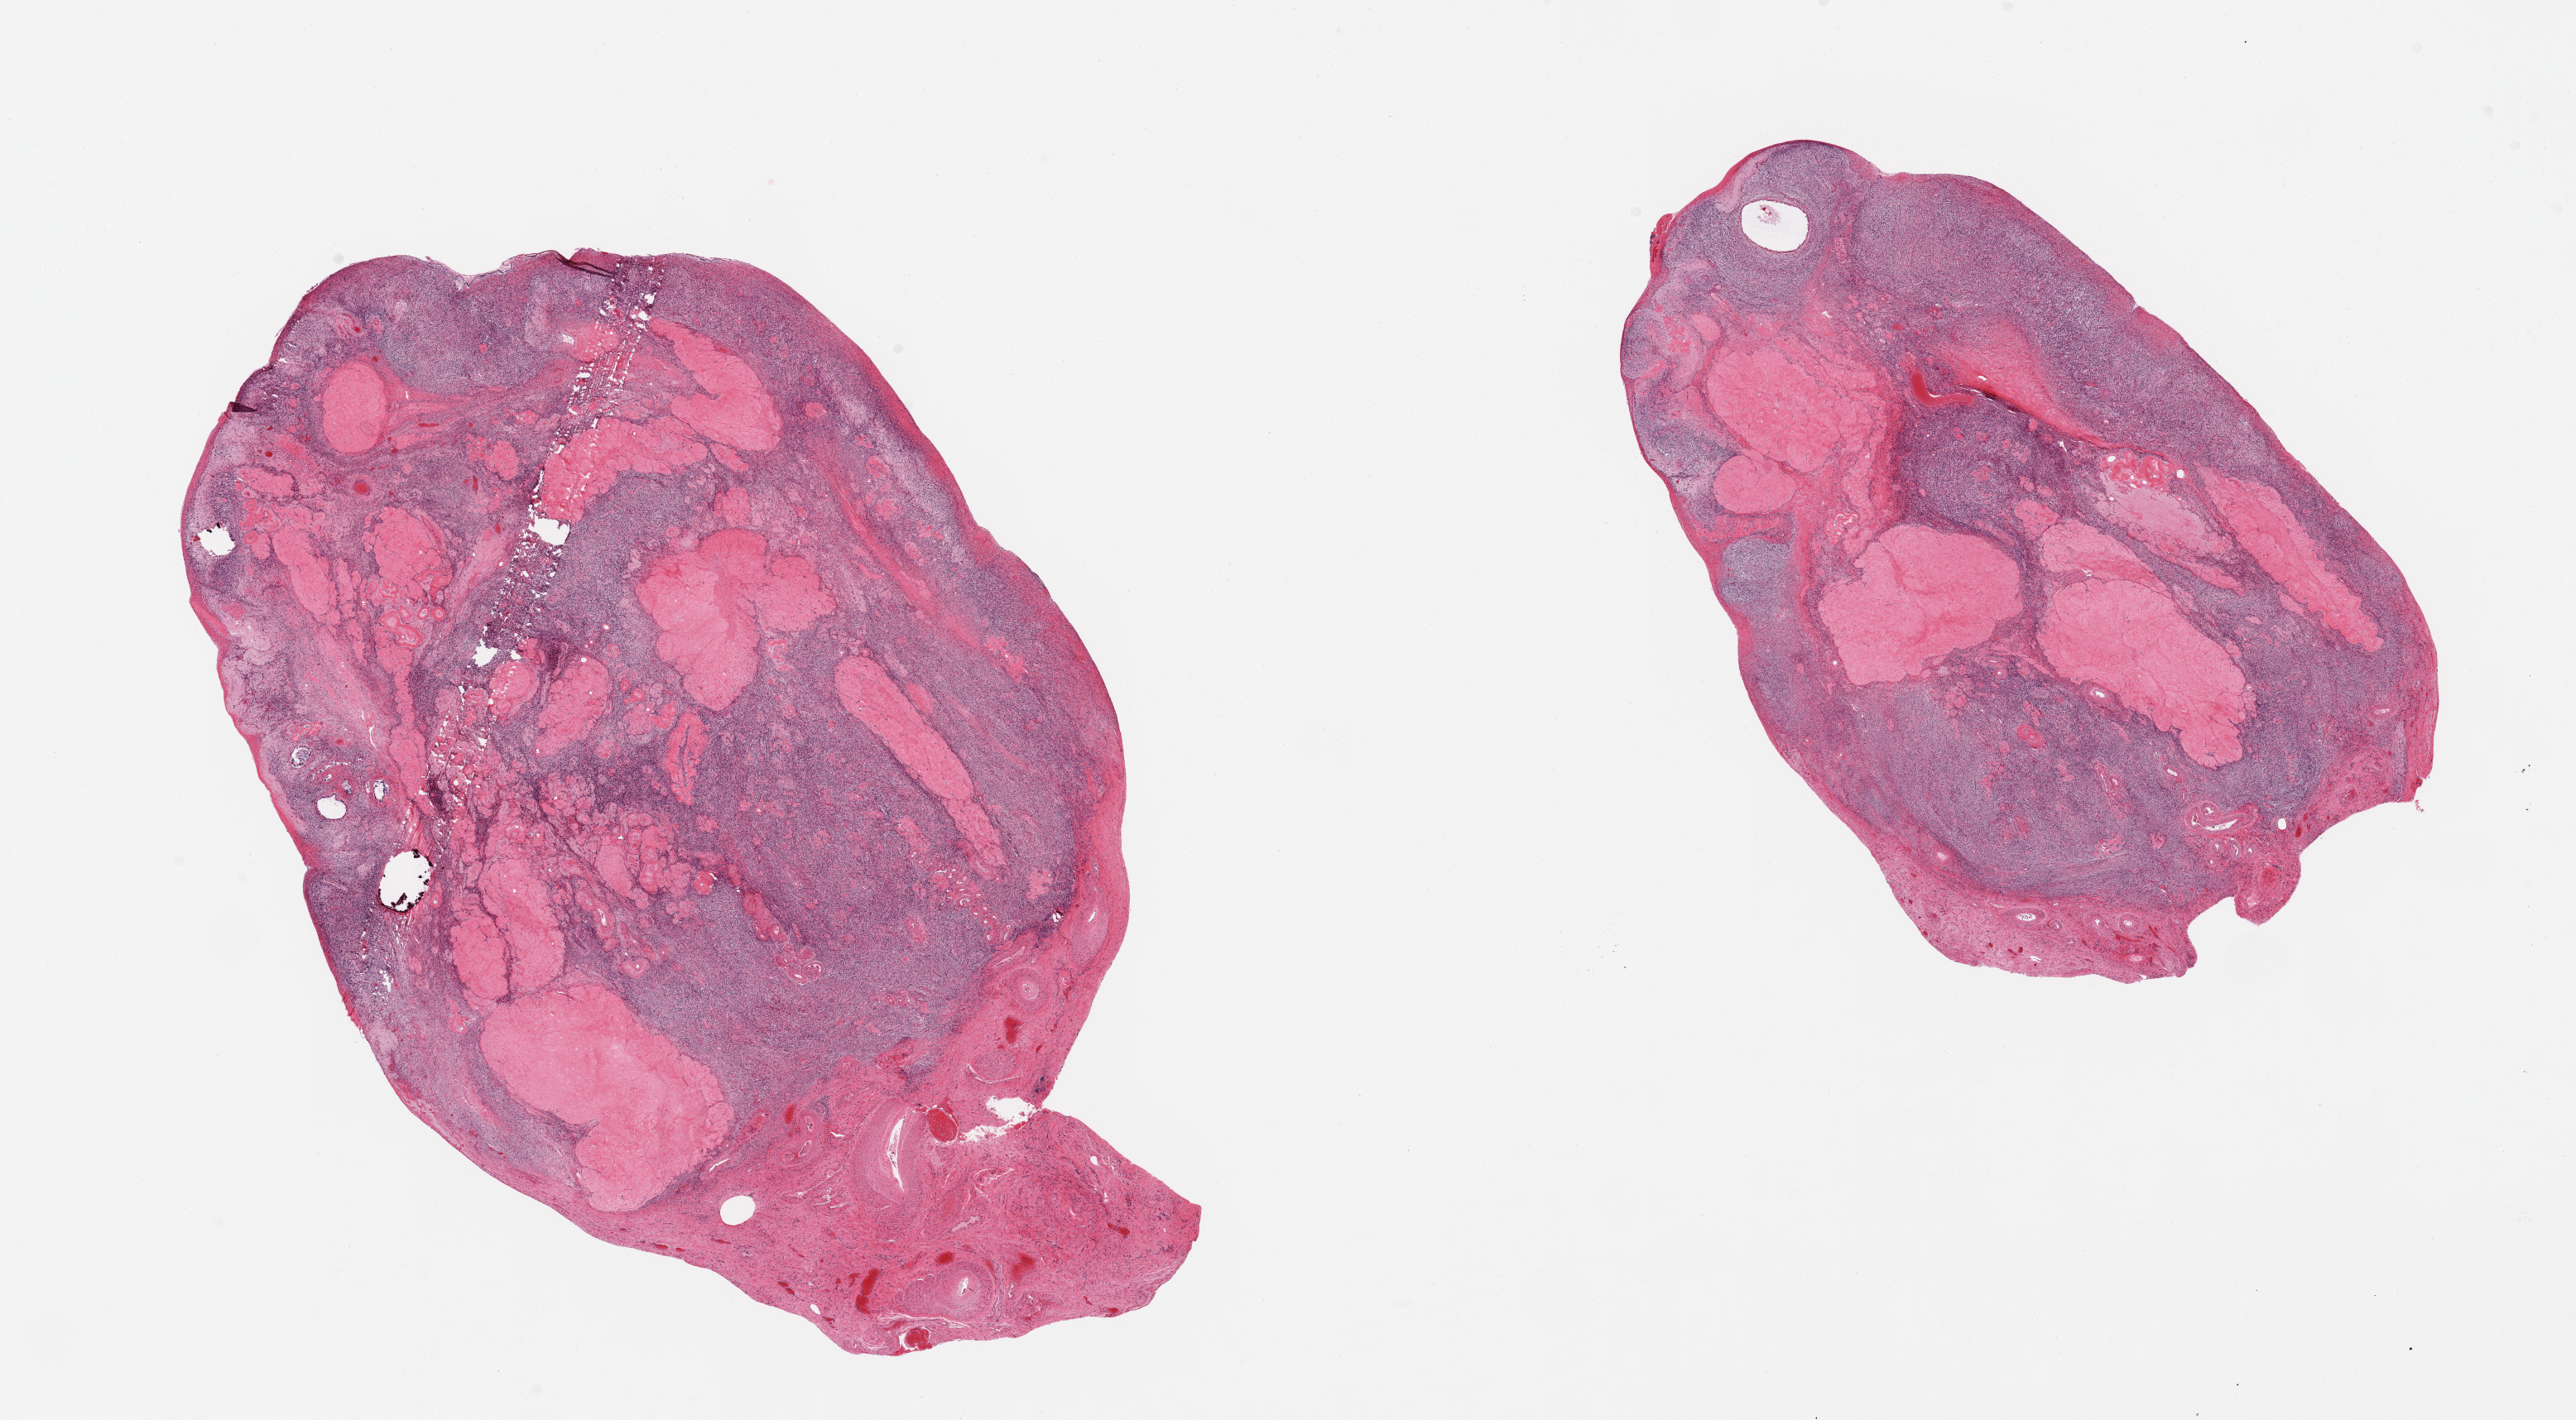
Digitized hematoxylin and eosin (H&E)-stained section, a low-resolution overview of the entire scanned area, about 24.6 x 13.6 mm, PAXgene-fixed paraffin-embedded (PFPE) section, section of ovary (target tissue), tissue donor sample. Donor sex: female.
Reviewer comment on this tissue sample: 2 pieces; atrophic with large corpora albicans comprising 40%.